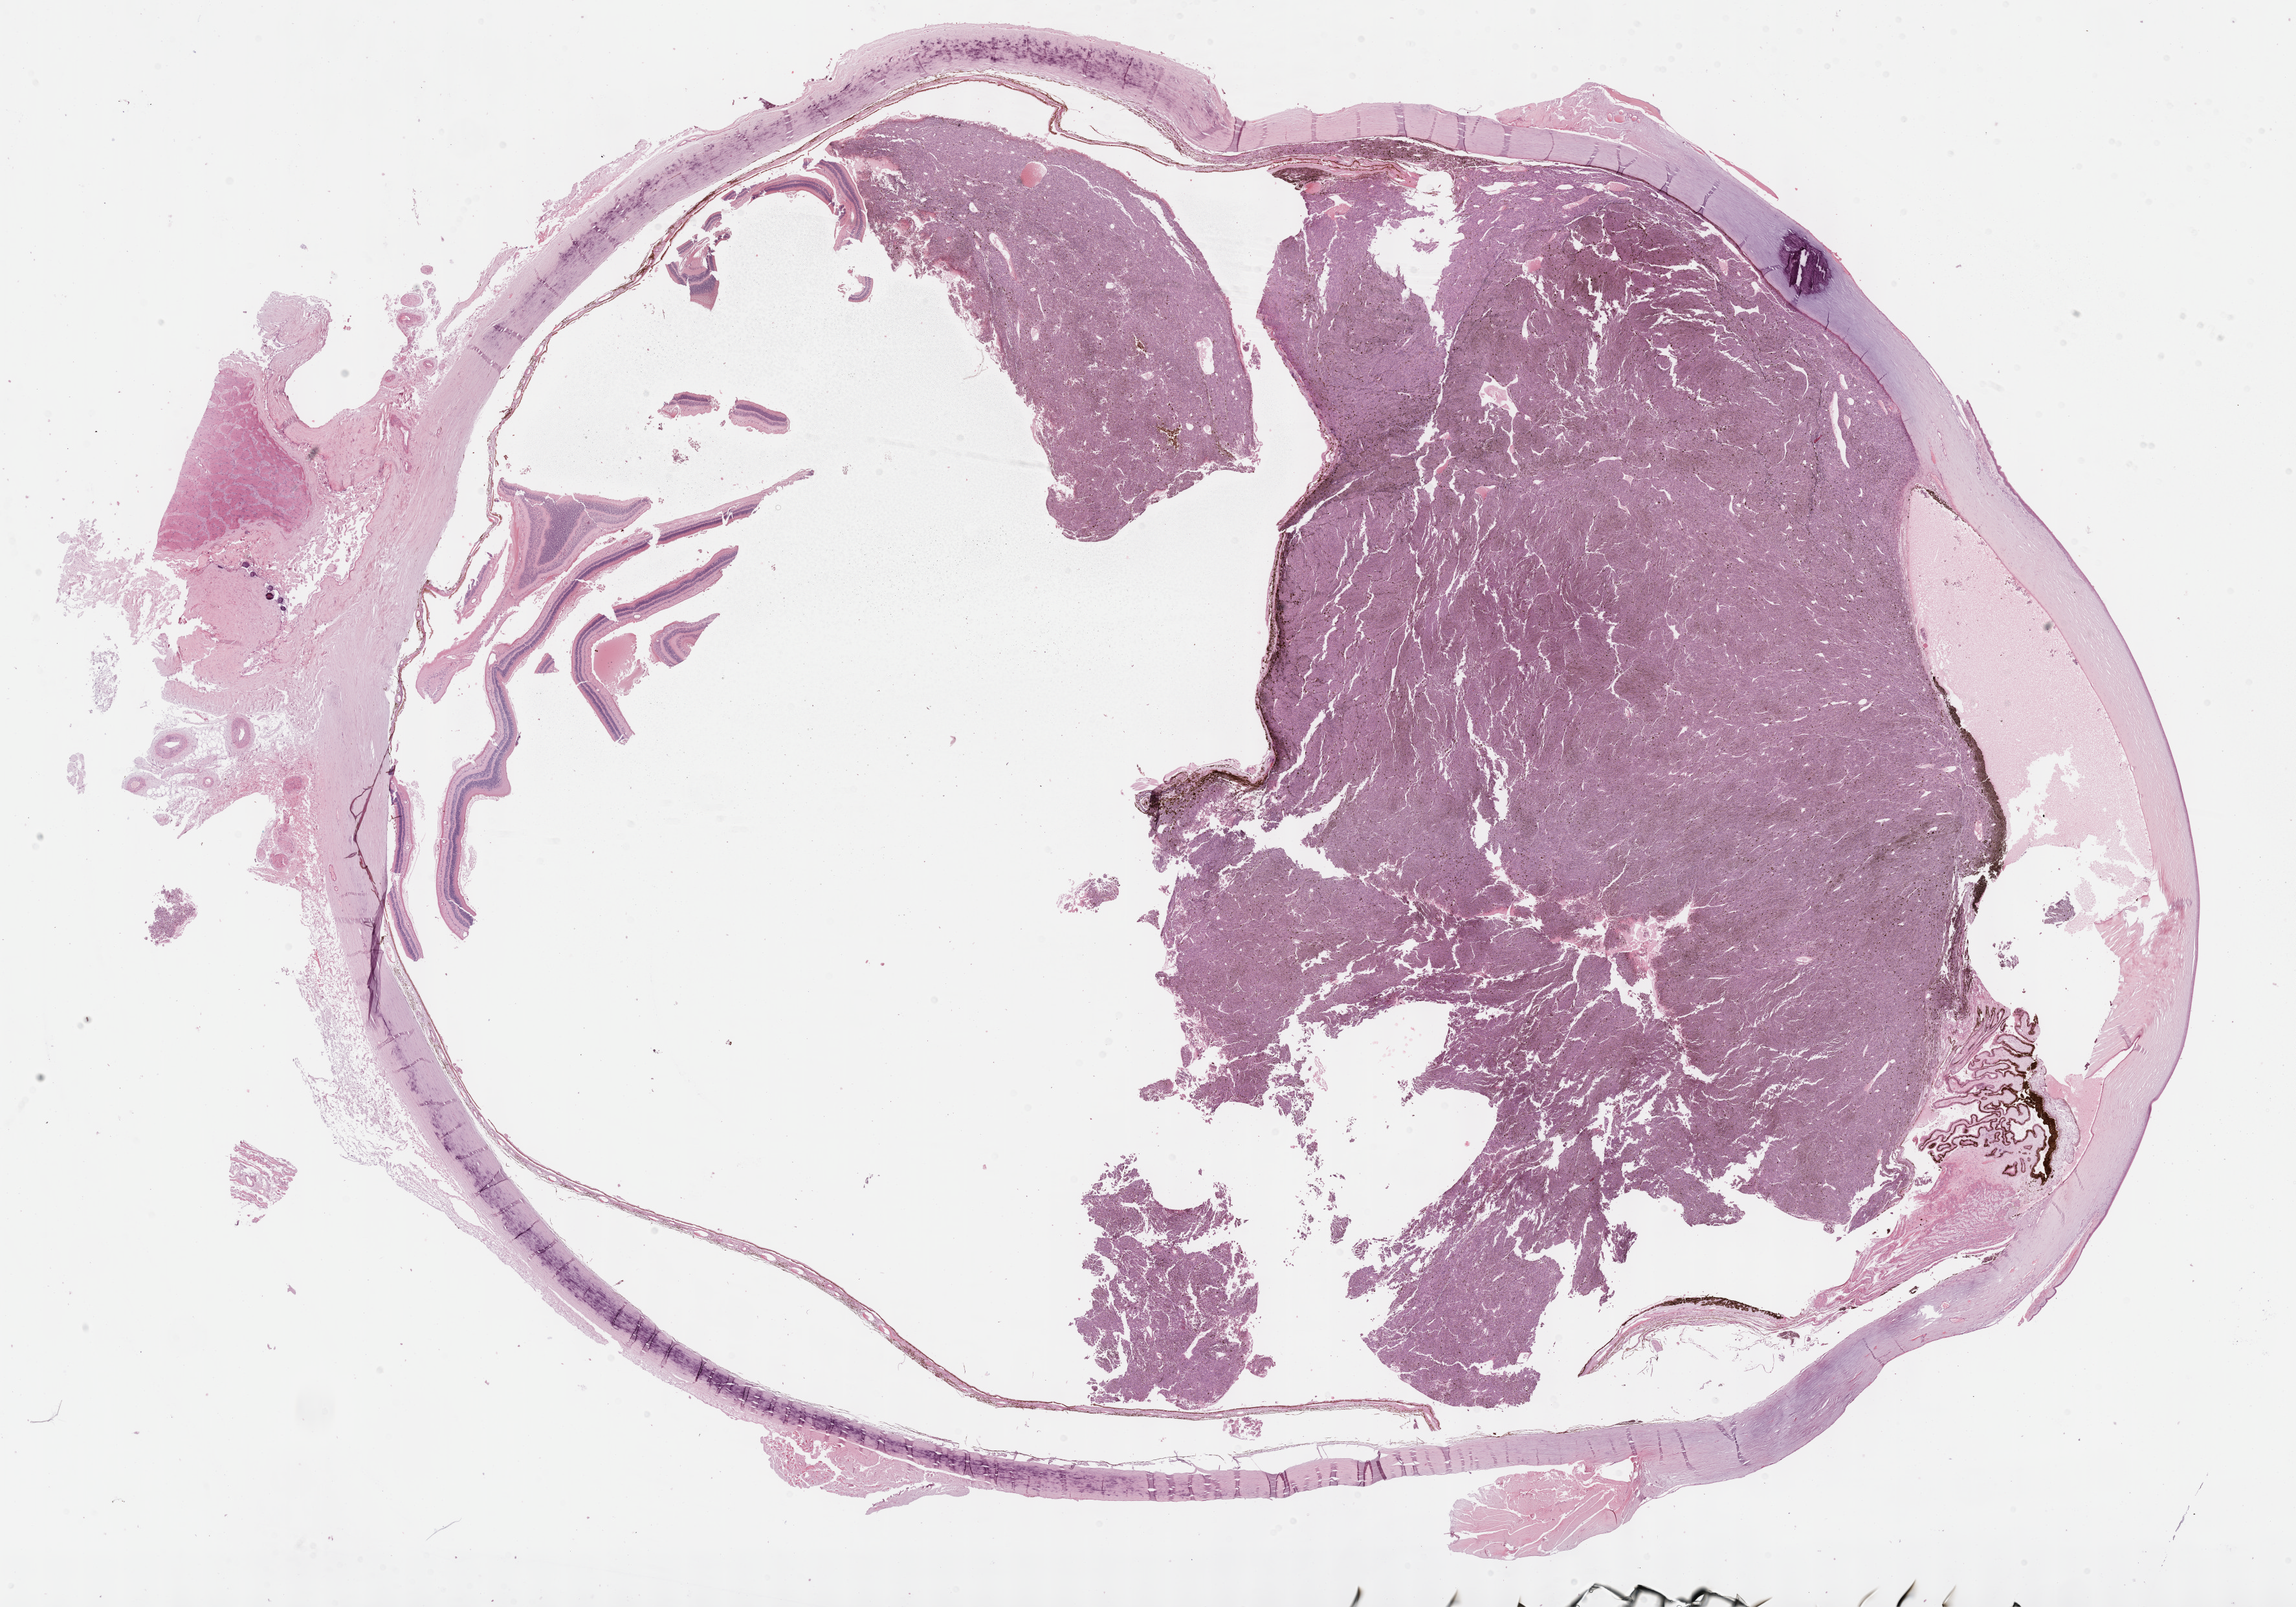
H&E whole-slide image — whole scanned area (about 28.7 x 20.1 mm, from a 40x scan) shown as a low-resolution overview; formalin-fixed paraffin-embedded (FFPE) diagnostic section; primary tumour sample from the uvea. Female, age 85 years at initial diagnosis.
AJCC pathologic stage: IV (7th edition). Laterality: right. Diagnosis: Mixed epithelioid and spindle cell melanoma (choroid).